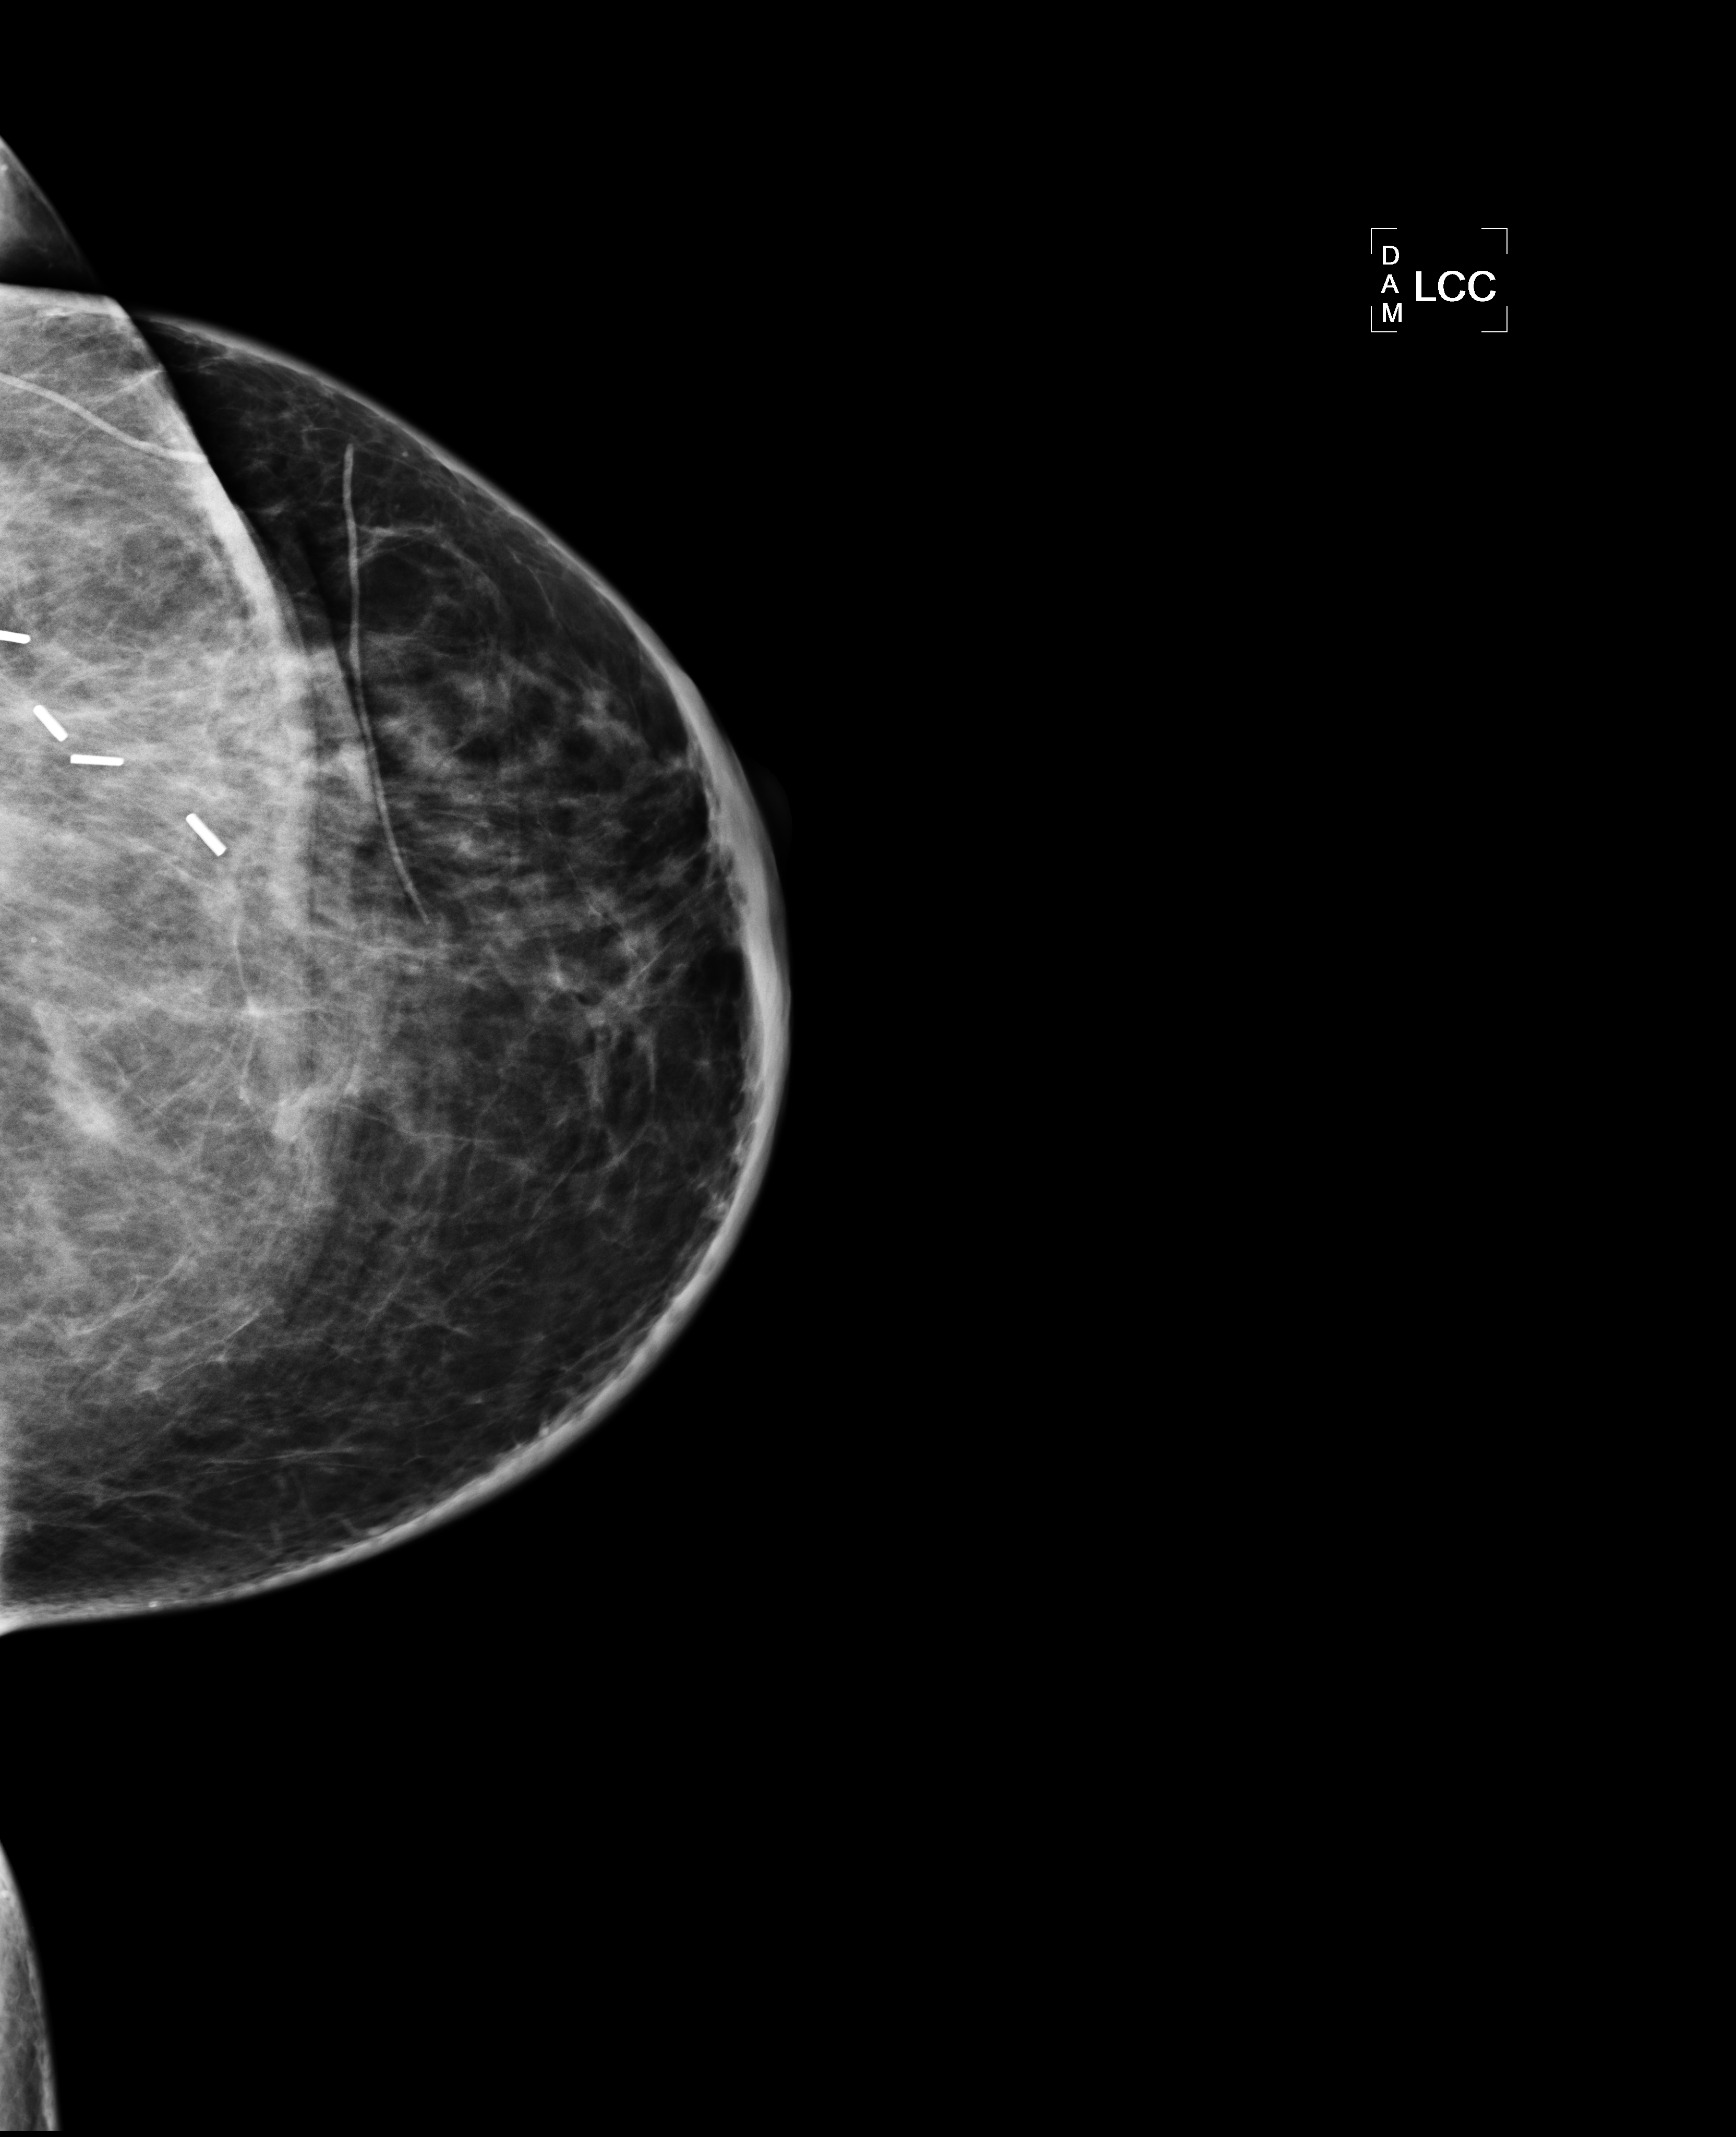
Mammogram, left breast, CC view; patient in her 50s.
Pathology recorded for this patient (not read from this image): pathology diagnosis: Invasive ductal CA (left breast); receptor status (as recorded): ER pos, PR pos (weak), HER2 neg; Ki-67 (as recorded): intermed prolif; pathology report notes: re-bx [date] was scar tissue from RT rx.